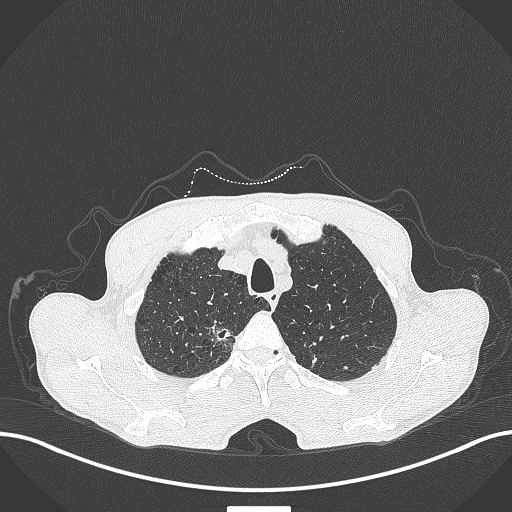
Chest CT, one axial slice; position 365 of 445 along the scan axis; reconstruction kernel B70f; 120 kVp; lung window (W 1500 / L -600 HU); 1 mm slice thickness; 512 × 512 image matrix. Male patient, age 70 years. From the clinical record (not read from this slice): clinical TNM (as recorded): T1a N0 M0.
Outlined on this slice (rectangle marked by the reading radiologist):
- lung tumour (recorded histology: adenocarcinoma): bounding box [x1, y1, x2, y2] px = [203, 318, 235, 346]